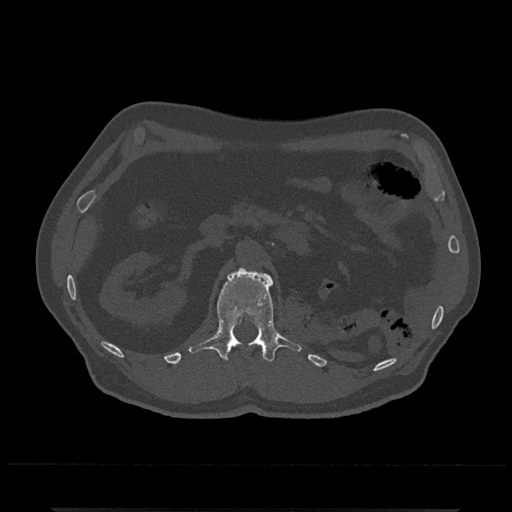
CT including the spine, one axial slice. Position 367 of 797 along the scan axis. Reconstruction kernel Br40s/3. Bone window (W 1800 / L 400 HU). 512 × 512 image matrix, field of view 393 × 393 mm. Patient: male, 67 years. From the clinical record (not read from this slice): primary cancer: prostate.
Outlined on this slice (semi-automatic segmentation, software-assisted and operator-edited):
- L1 vertebra: box from (x=188, y=268) to (x=302, y=362) px
- T12 vertebra: (x=260, y=345)–(x=262, y=347)